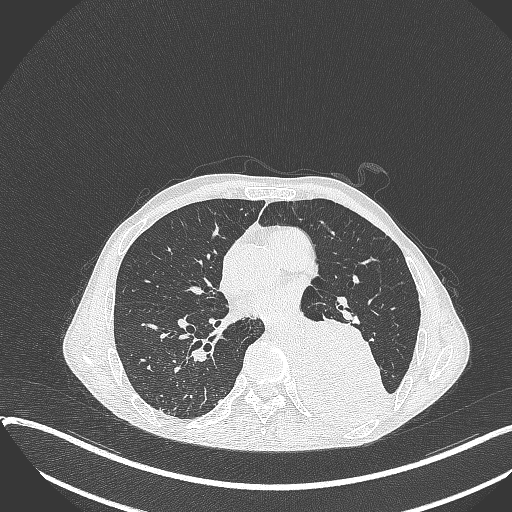
Chest CT, one axial slice; position 173 of 401 along the scan axis; reconstruction kernel B70f; 120 kVp; lung window (W 1500 / L -600 HU); 1 mm slice thickness; 512 × 512 image matrix, field of view 400 × 400 mm. Male patient, age 57 years. Case-level facts recorded for this patient, not image findings: clinical TNM (as recorded): T4 N0 M0.
Structures marked on this image (bounding box drawn by a radiologist):
- lung tumour (recorded histology: squamous cell carcinoma): bounding box <294,310,390,430> (left, top, right, bottom; pixels)